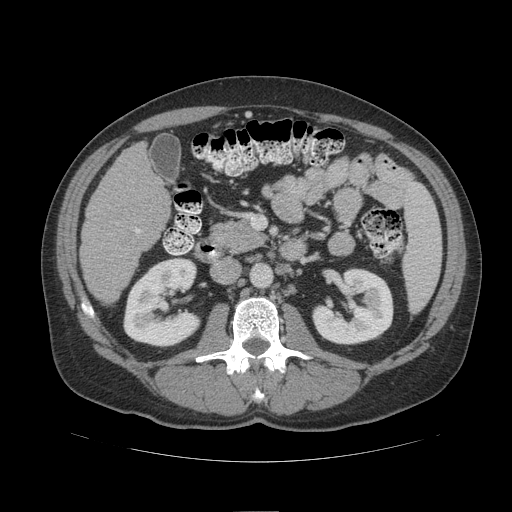
Contrast-enhanced abdominal CT (liver protocol), one axial slice; slice 43 of 109 in the series (ordered by position); reconstruction kernel STANDARD; 140 kVp; soft-tissue window (W 400 / L 40 HU); 2.5 mm slice thickness; 512 × 512 image matrix, field of view 420 × 420 mm. From the clinical record (not read from this slice): diagnosis: hepatocellular carcinoma (patient treated with transarterial chemoembolisation; whether this scan precedes or follows treatment is not stated here); TNM stage (as recorded): Stage-IIIB; Child-Pugh class: A; tumour nodularity: multinodular.
Annotated regions visible in this slice (semi-automatic segmentation, software-assisted and operator-edited):
- liver parenchyma outside the tumour (the mass and vessels are separate outlines, so this box may not span the whole liver): bounding box (x1, y1, x2, y2) in pixels: (80, 142, 170, 302)
- liver vessels: (135, 228, 140, 233)